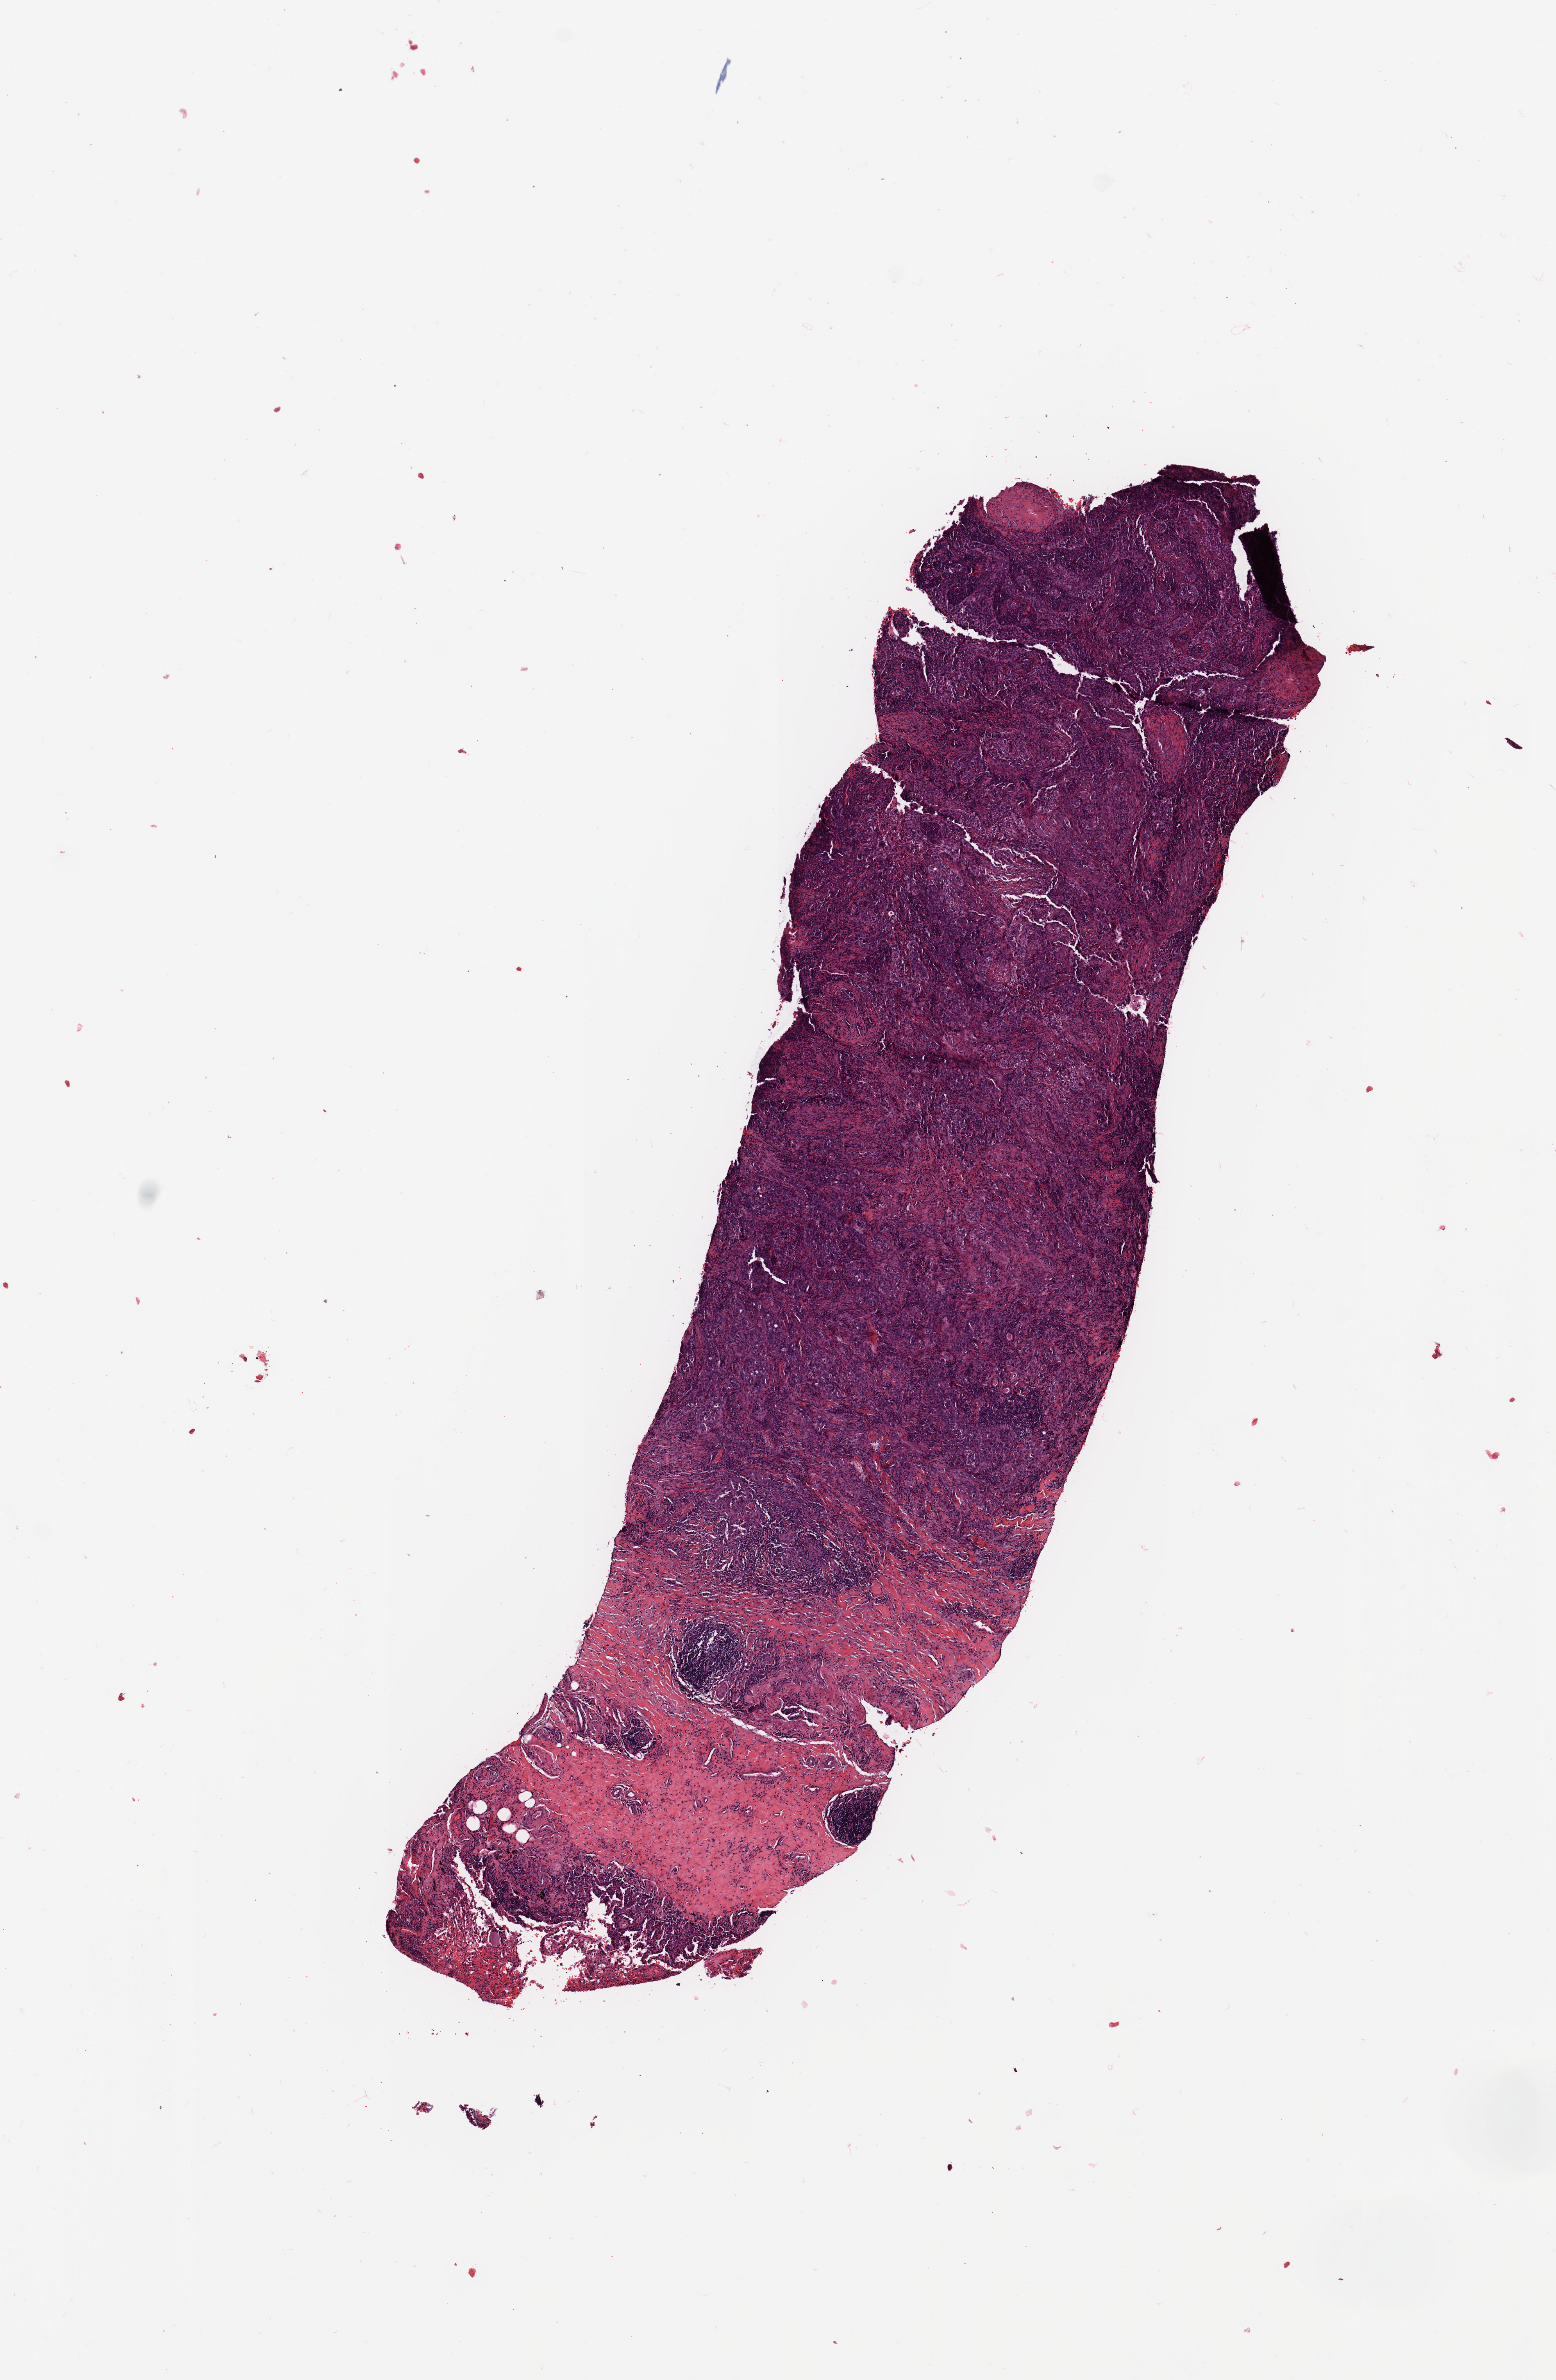
Whole-slide histology image, Hematoxylin and eosin (H&E) stained — a low-resolution overview of the entire scanned area, about 7.9 x 12.0 mm; tumour tissue sample, sampled site: lung. Patient: male, age 88 years. Histologic grade: G3 (poorly differentiated). Slide review estimates, as recorded: tumour nuclei 70%, necrosis 2%.
Histologic diagnosis: Squamous cell carcinoma, NOS. AJCC pathologic stage: IIA. Primary tumour site (as recorded): left lower lobe.